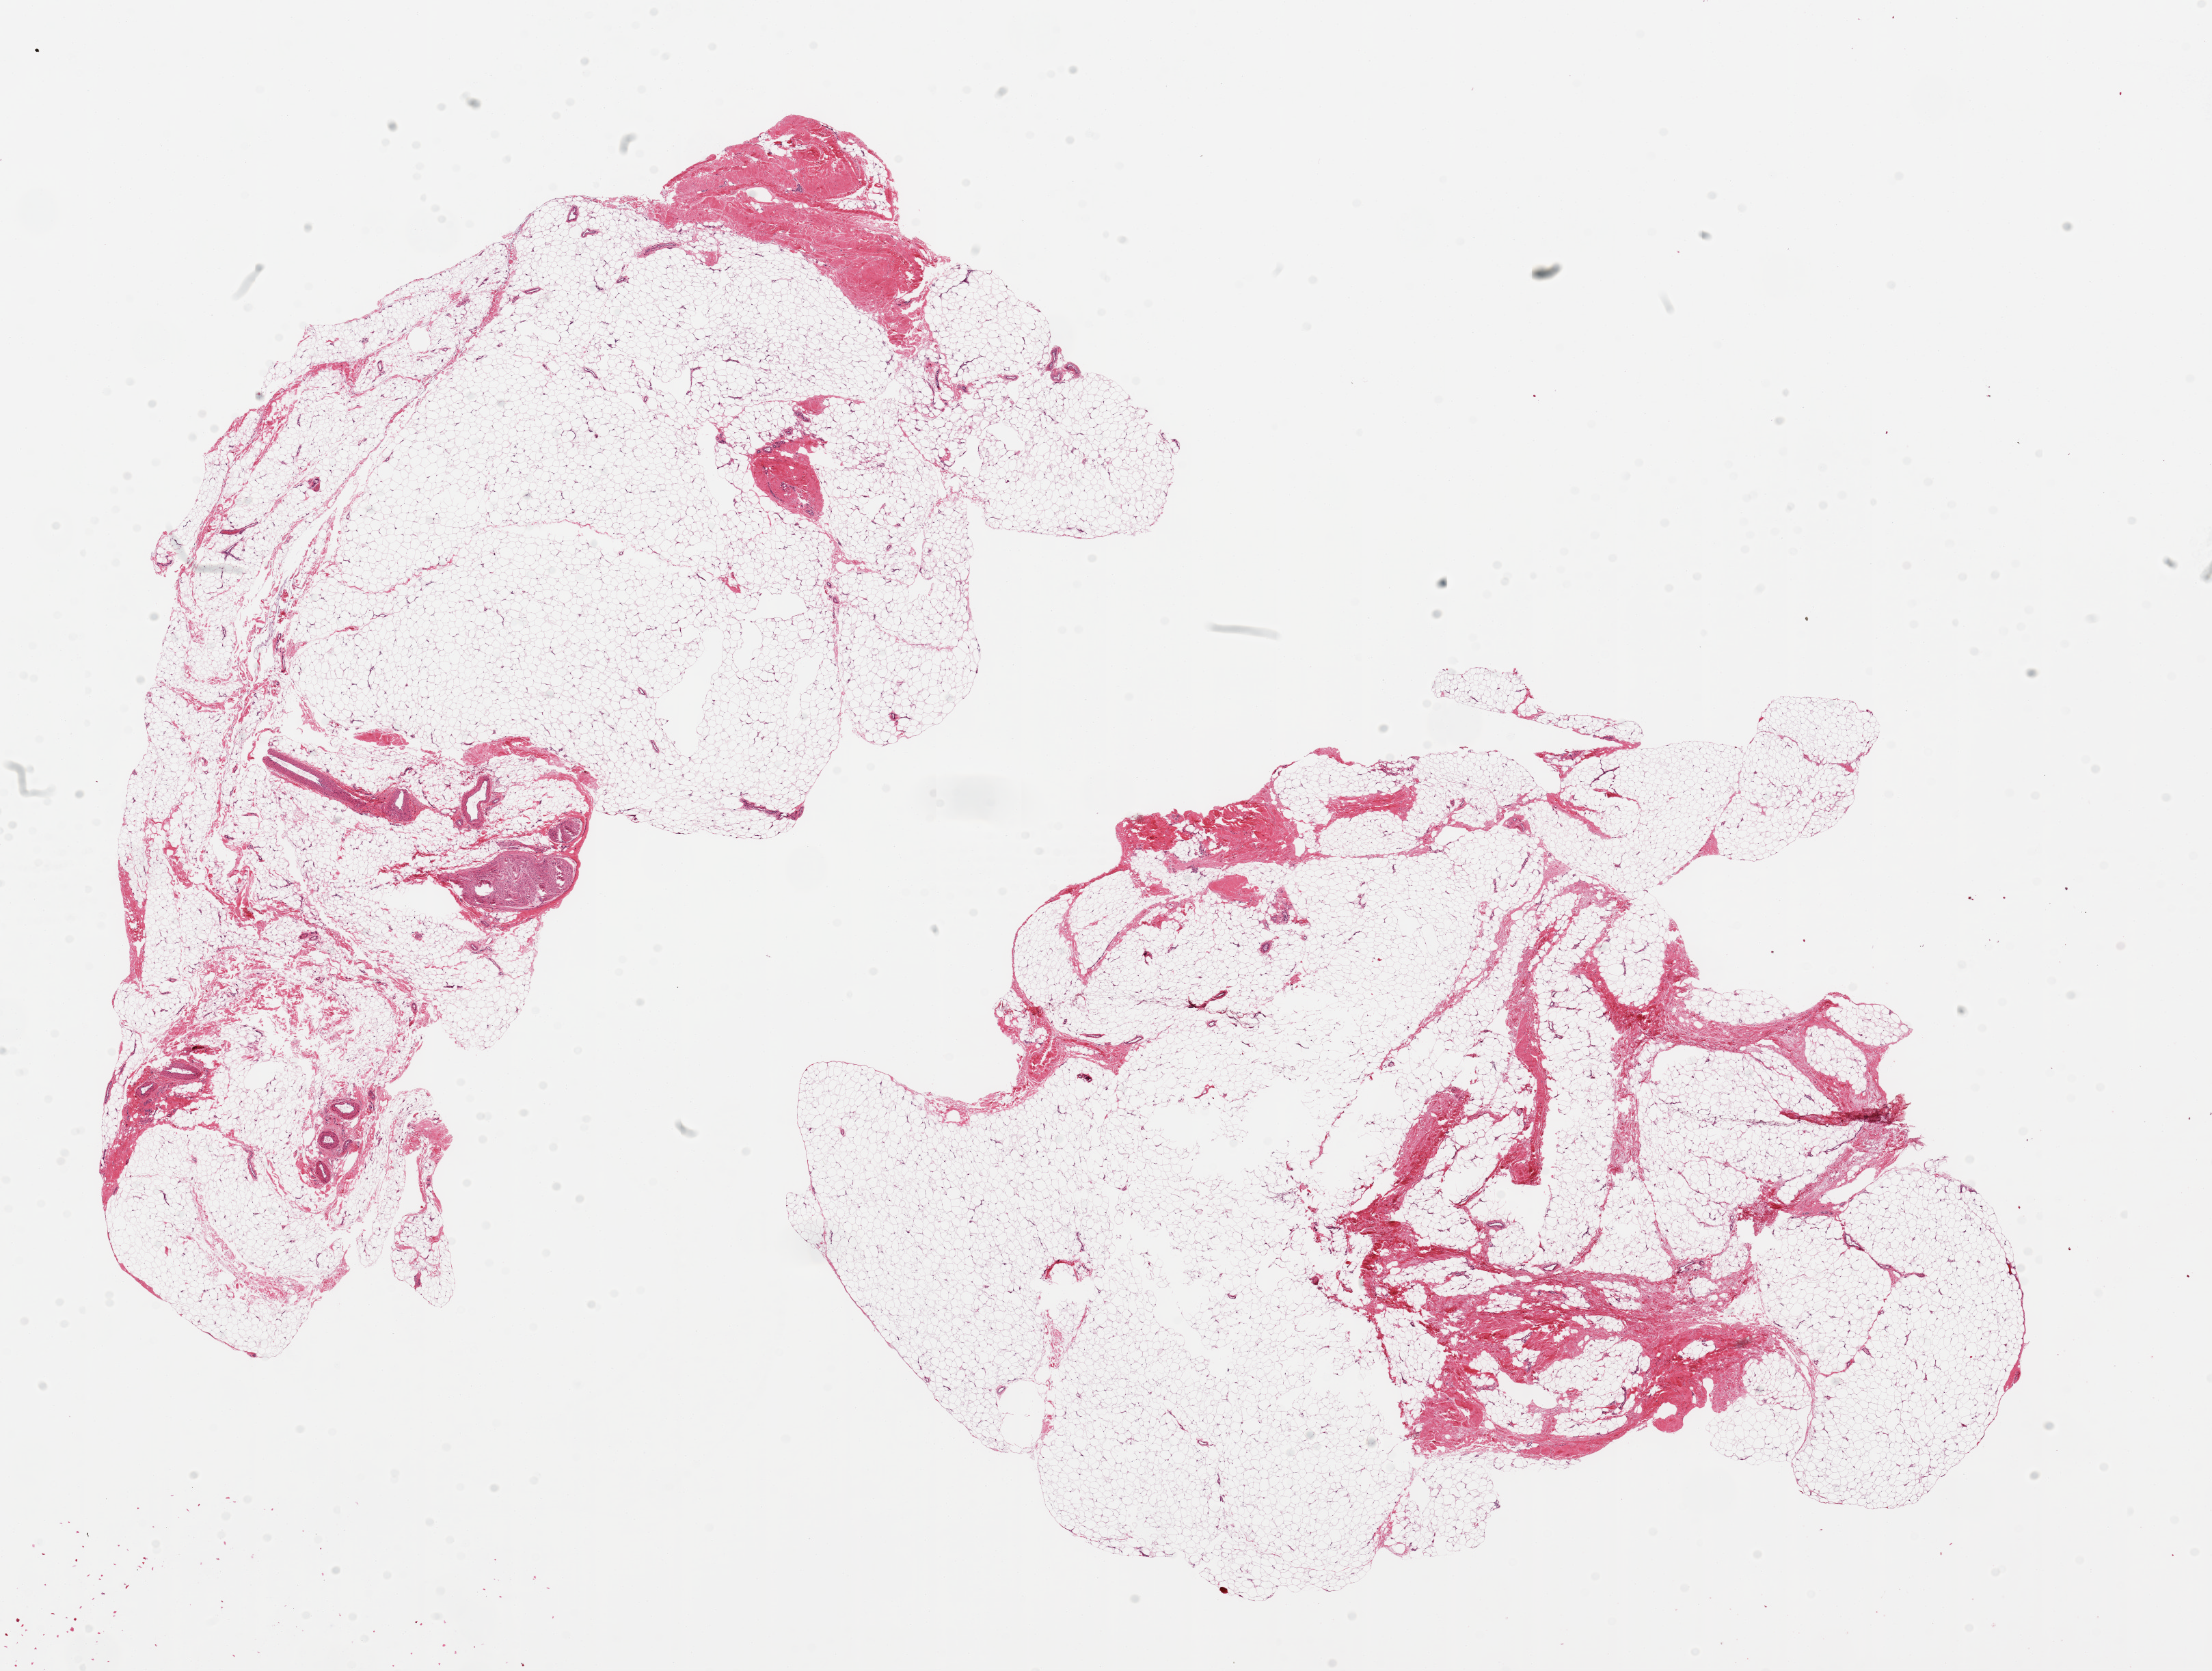
Digitized haematoxylin and eosin-stained section, low-resolution overview of the scanned area, about 25.6 x 19.3 mm (from a 20x scan); PAXgene-fixed, paraffin-embedded tissue; target tissue: adipose tissue; donor tissue sample. Donor: male.
Review note (as recorded): 2 ~13x9mm pieces. Well fixed.